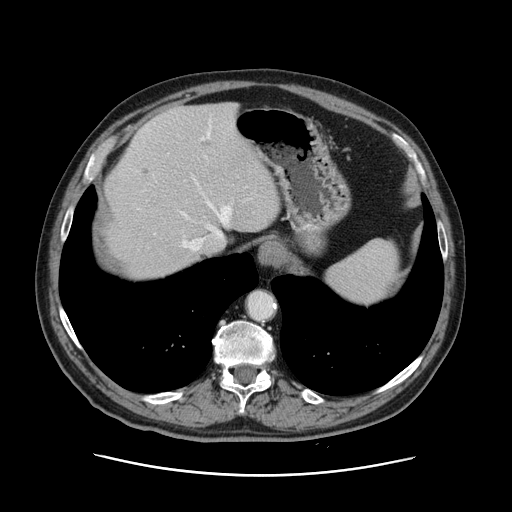
Contrast-enhanced abdominal CT, one axial slice; position 105 of 141 along the scan axis; 120 kVp; soft-tissue window (W 400 / L 40 HU); 2.5 mm slice thickness; 512 × 512 image matrix. Male patient, age 72 years. From the clinical record (not read from this slice): diagnosis: colorectal cancer liver metastases, imaged before liver resection; multiple liver metastases: yes; largest metastasis: 5.4 cm.
Annotated regions visible in this slice (outlined manually by an expert reader):
- hepatic veins: box from (x=154, y=133) to (x=231, y=251) px
- liver: (x=104, y=102)–(x=279, y=282)
- planned liver remnant (the part of the liver to remain after resection): (x=127, y=103)–(x=279, y=282)
- portal vein (with intrahepatic branches): (x=192, y=121)–(x=230, y=249)